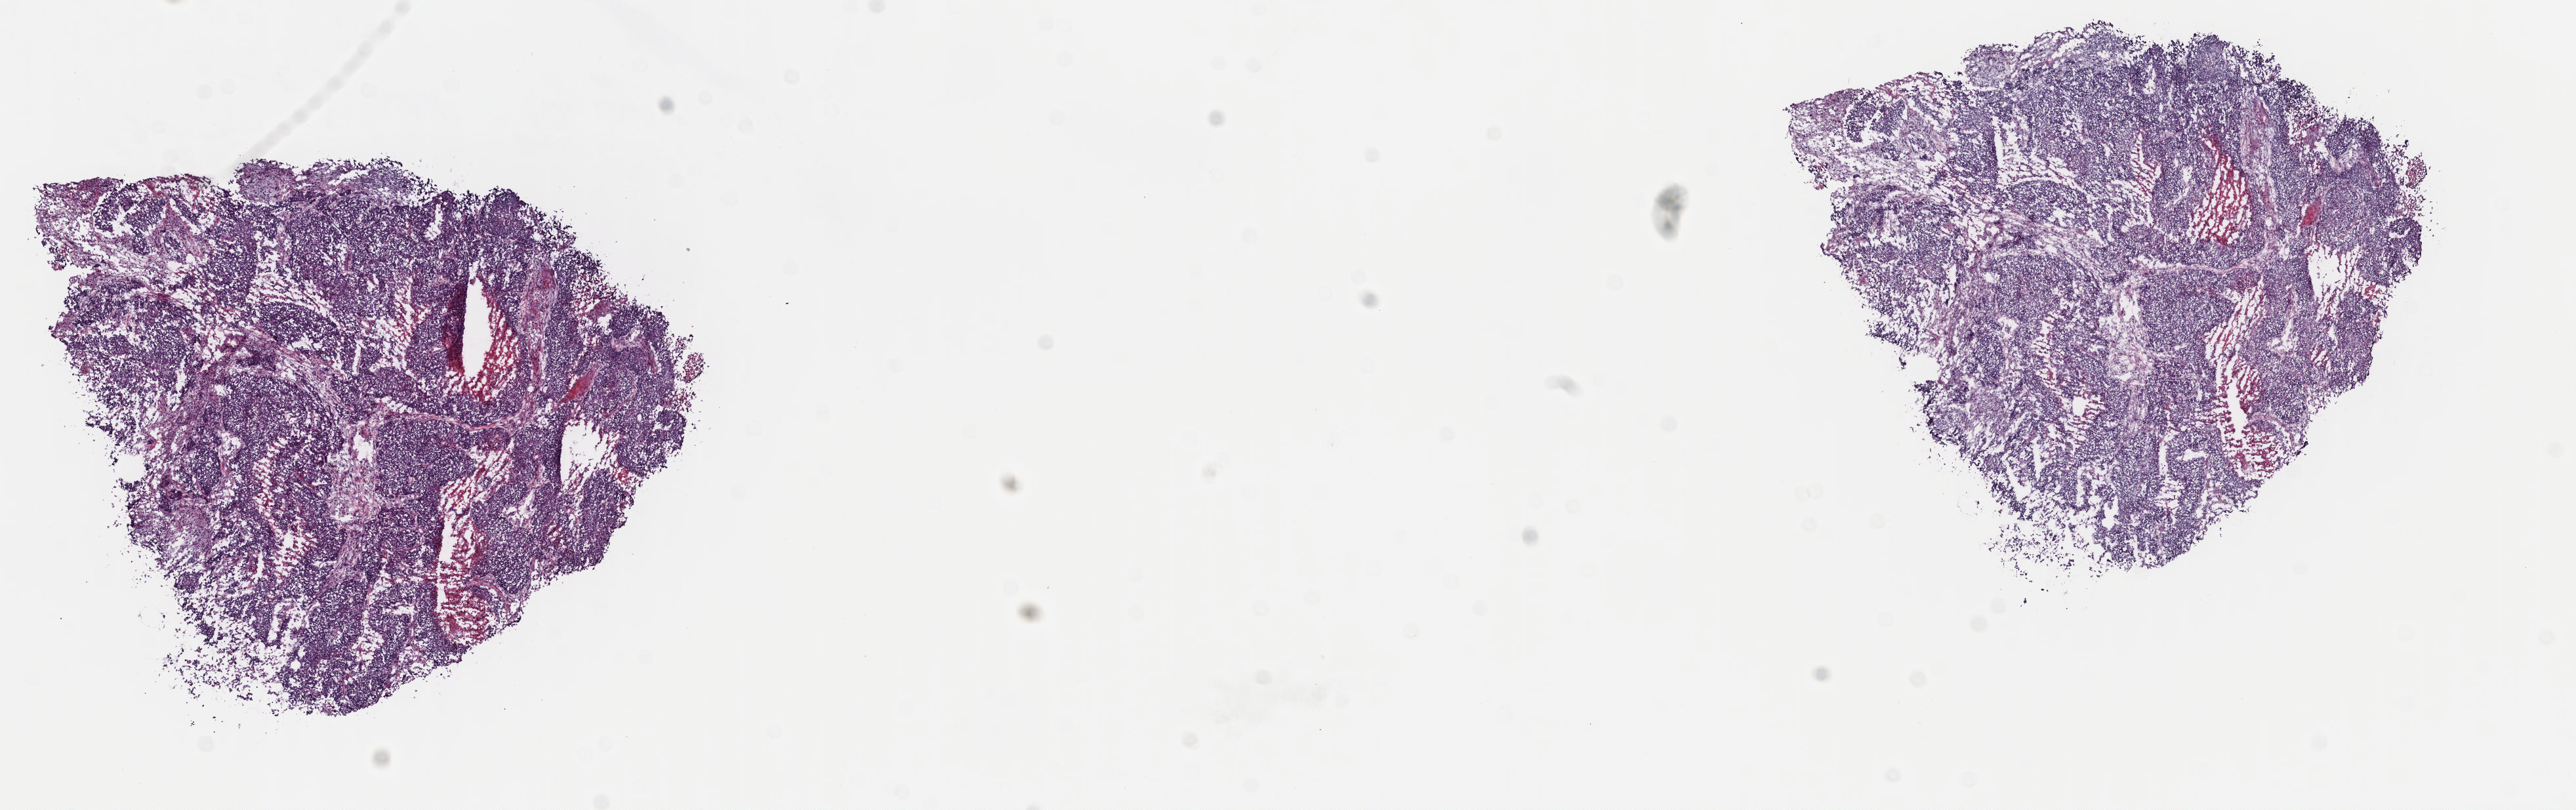
Whole-slide histology image, H&E, a low-resolution overview of the entire scanned area, about 15.5 x 4.9 mm (from a 40x scan). Frozen section from the top of the tissue portion. Cervix, primary tumour sample. Female, age 53 years at initial diagnosis. Histologic grade: G2 (moderately differentiated). Pathologist review of this section (percent, as recorded): tumour cells 90%, tumour nuclei 90%, normal cells 0%, stromal cells 5%, necrosis 5%. Infiltration values recorded for this section: lymphocyte infiltration 40%, monocyte infiltration 20%, neutrophil infiltration 20%.
FIGO stage: IVB. Diagnosis: Squamous cell carcinoma, NOS (cervix uteri).